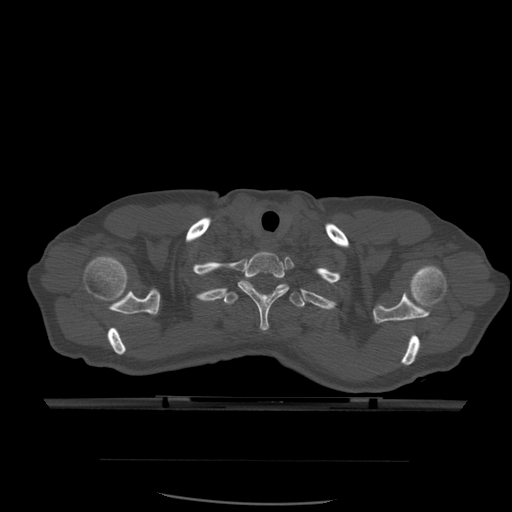
CT including the spine, one axial slice. Slice 467 of 574 in the series (ordered by position). Bone window (W 1800 / L 400 HU). 1.25 mm slice thickness. 512 × 512 image matrix, field of view 392 × 392 mm. Patient age 48 years. Case-level facts recorded for this patient, not image findings: primary cancer: lung; vertebrae with lytic lesions (as recorded): T11.
Outlined on this slice (semi-automatic segmentation, software-assisted and operator-edited):
- T1 vertebra: box from (x=238, y=251) to (x=289, y=331) px
- T2 vertebra: (x=223, y=279)–(x=306, y=308)